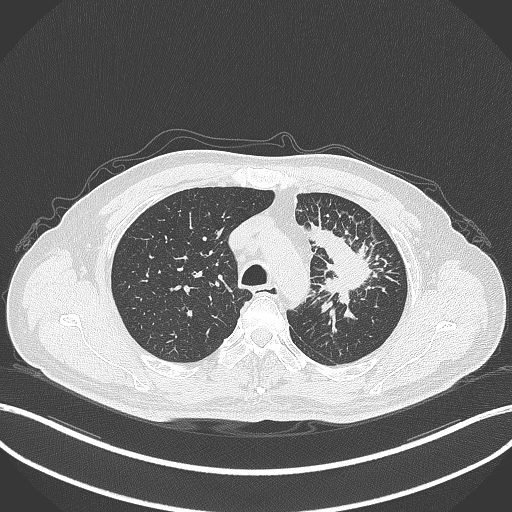
Chest CT, one axial slice. Slice 270 of 386 in the series (ordered by position). 120 kVp. Lung window (W 1500 / L -600 HU). 1 mm slice thickness. 512 × 512 image matrix, field of view 400 × 400 mm. Patient: male, 69 years. From the clinical record (not read from this slice): clinical TNM (as recorded): T2a N2 M0; histopathological grade: G2-3.
Outlined on this slice (rectangle marked by the reading radiologist):
- lung tumour (recorded histology: adenocarcinoma): bounding box <305,220,381,305> (left, top, right, bottom; pixels)